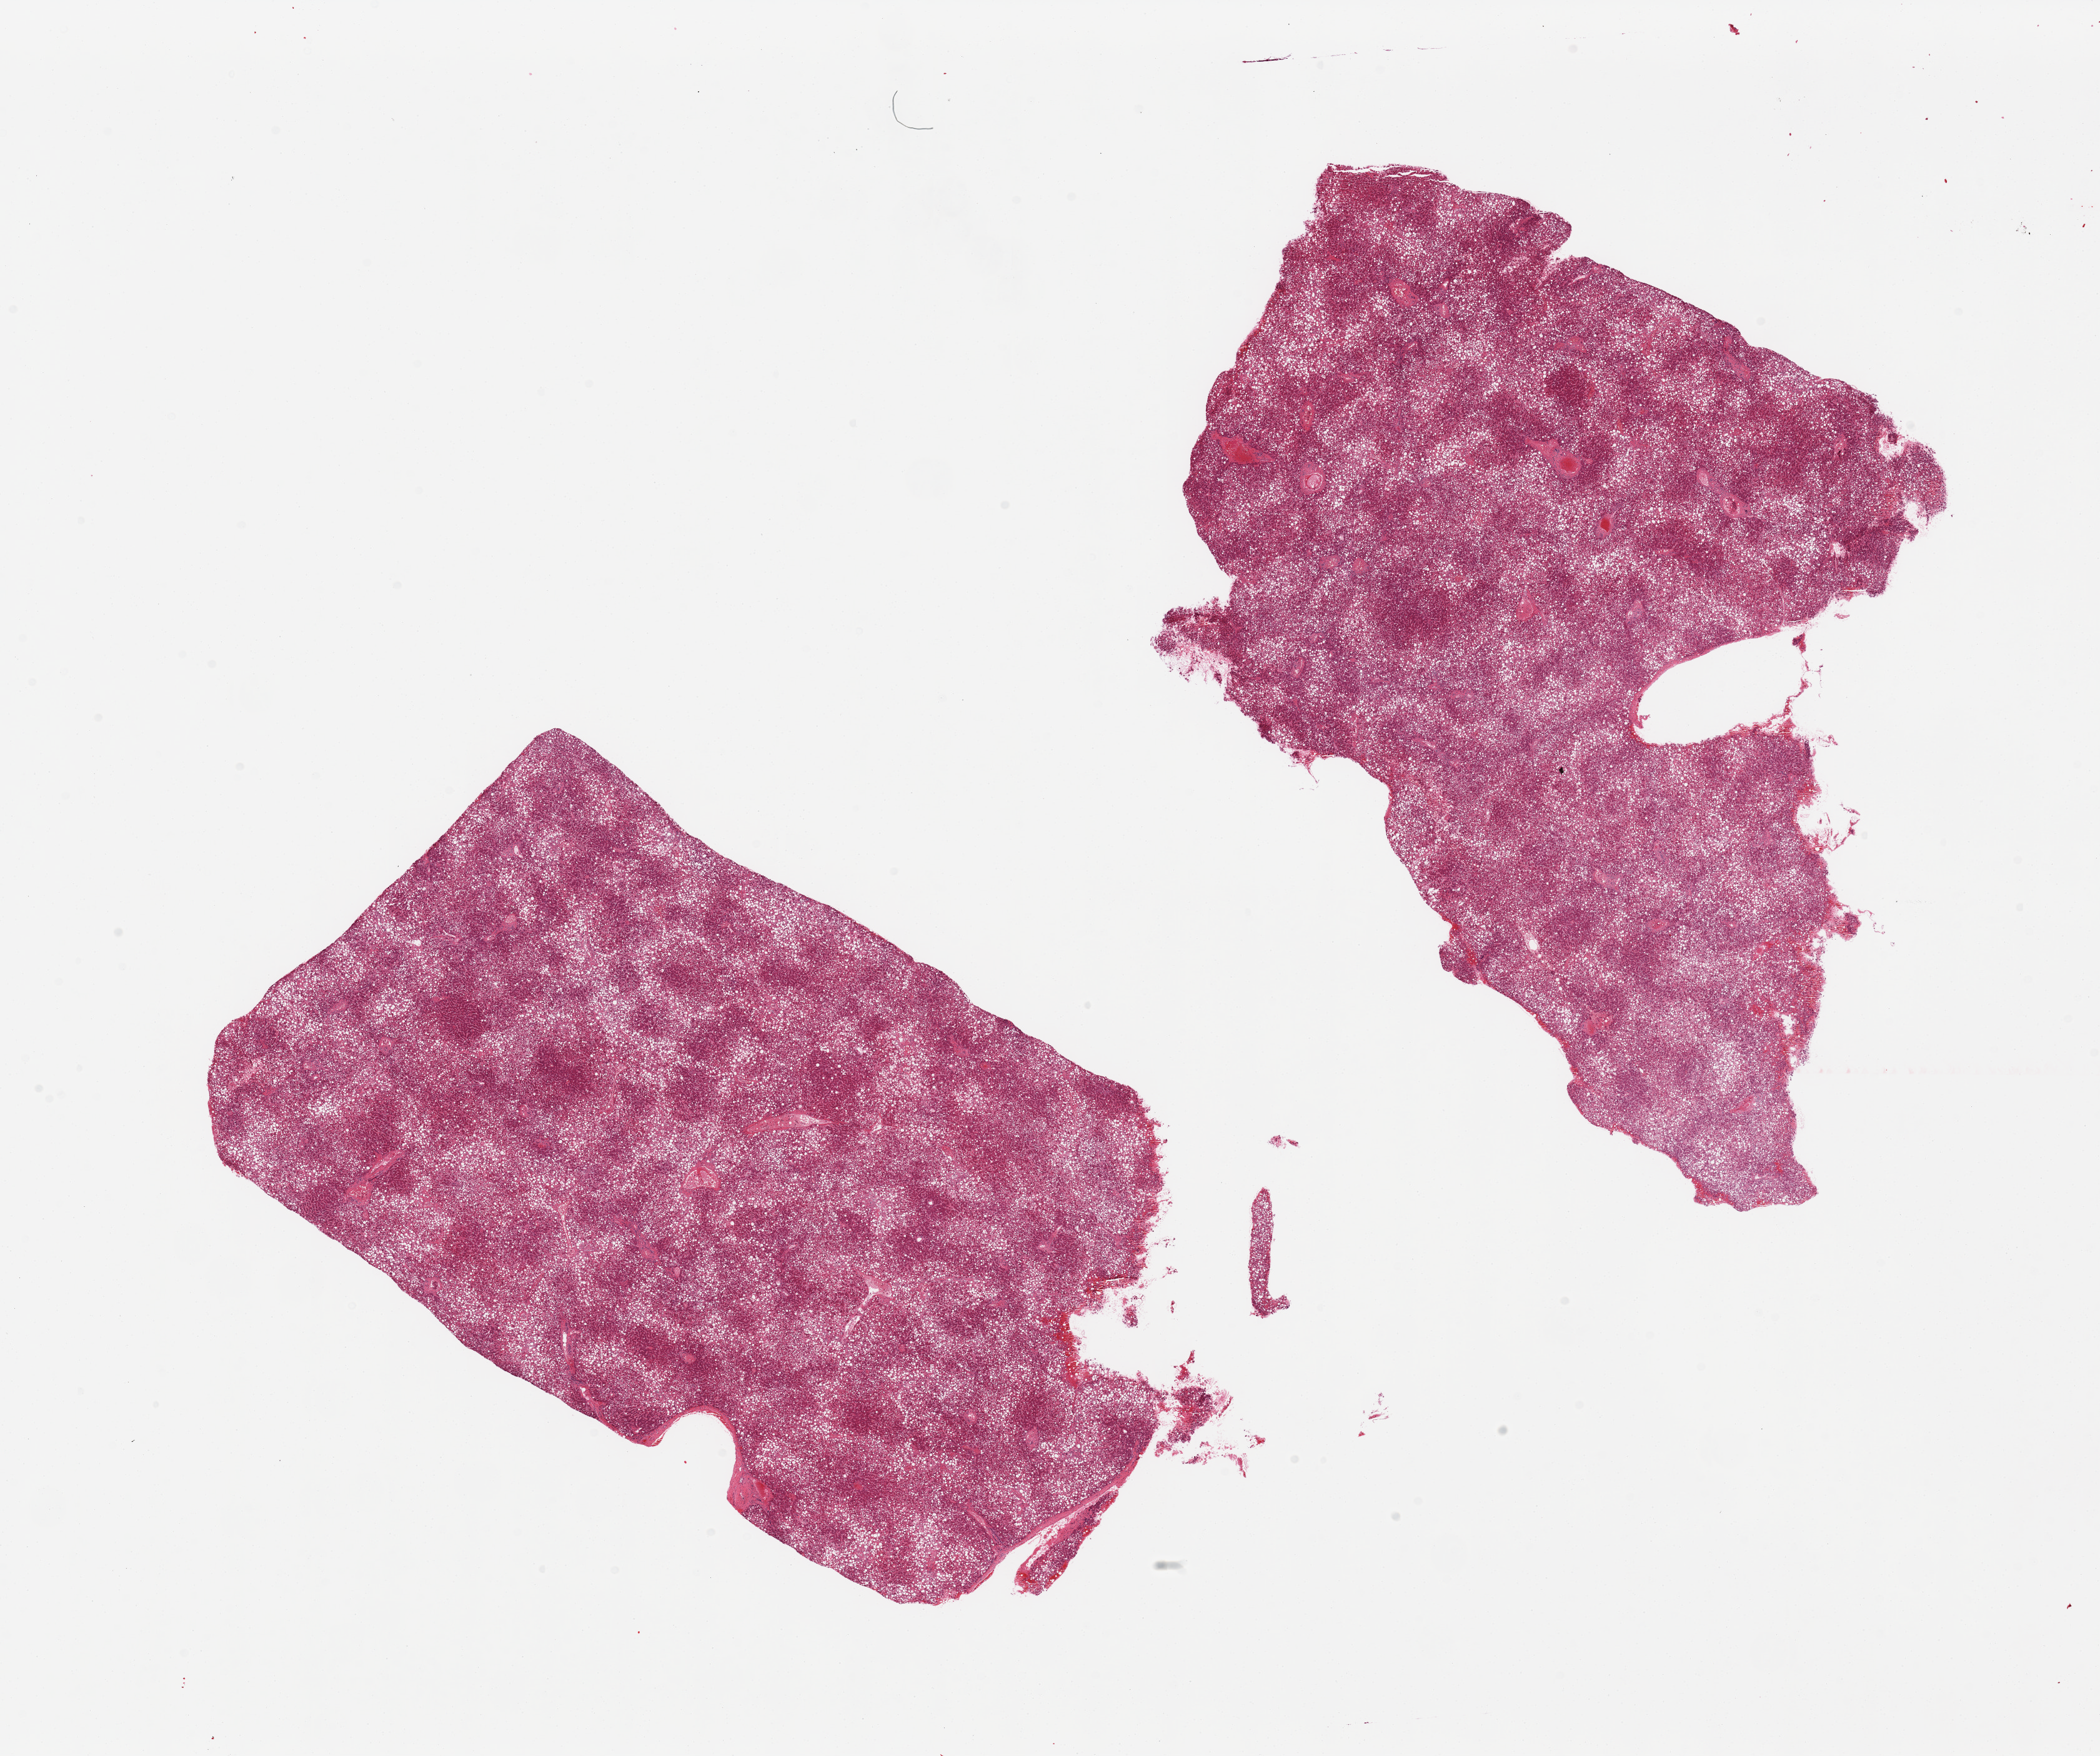
Whole-slide image, H&E stain, low-resolution overview of the scanned area, about 26.6 x 22.2 mm (acquisition: 20x scan); PAXgene-fixed, paraffin-embedded tissue; section of liver (target tissue); donor tissue sample.
• reviewer comment on this tissue sample: 2 pieces, diffuse macrovesicular steatosis involves ~80% of parenchyma